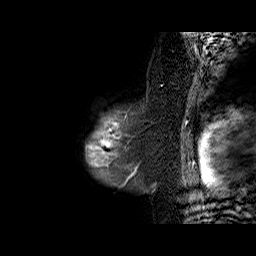
Breast MRI (dynamic contrast-enhanced), one sagittal slice; position 52 of 60 along the scan axis; dynamic contrast-enhanced series, time point 2 of 6 at this slice position (early post-contrast); 1.5 T; TE 6.3 ms, TR 32.4 ms; 4 mm slice thickness; 256 × 256 image matrix, field of view 200 × 200 mm. Female patient. From the clinical record (not read from this slice): setting: breast cancer imaged before/during neoadjuvant chemotherapy; receptor status: triple-negative.
Outlined on this slice (semi-automatic segmentation, software-assisted and operator-edited):
- analysis volume of interest (the breast-tissue region the enhancement analysis was run in; not a lesion): bounding box [x1, y1, x2, y2] px = [84, 98, 155, 187]
- tumour enhancement mask (voxels above the 100 % enhancement threshold inside the analysis volume of interest): [85, 117, 131, 176]